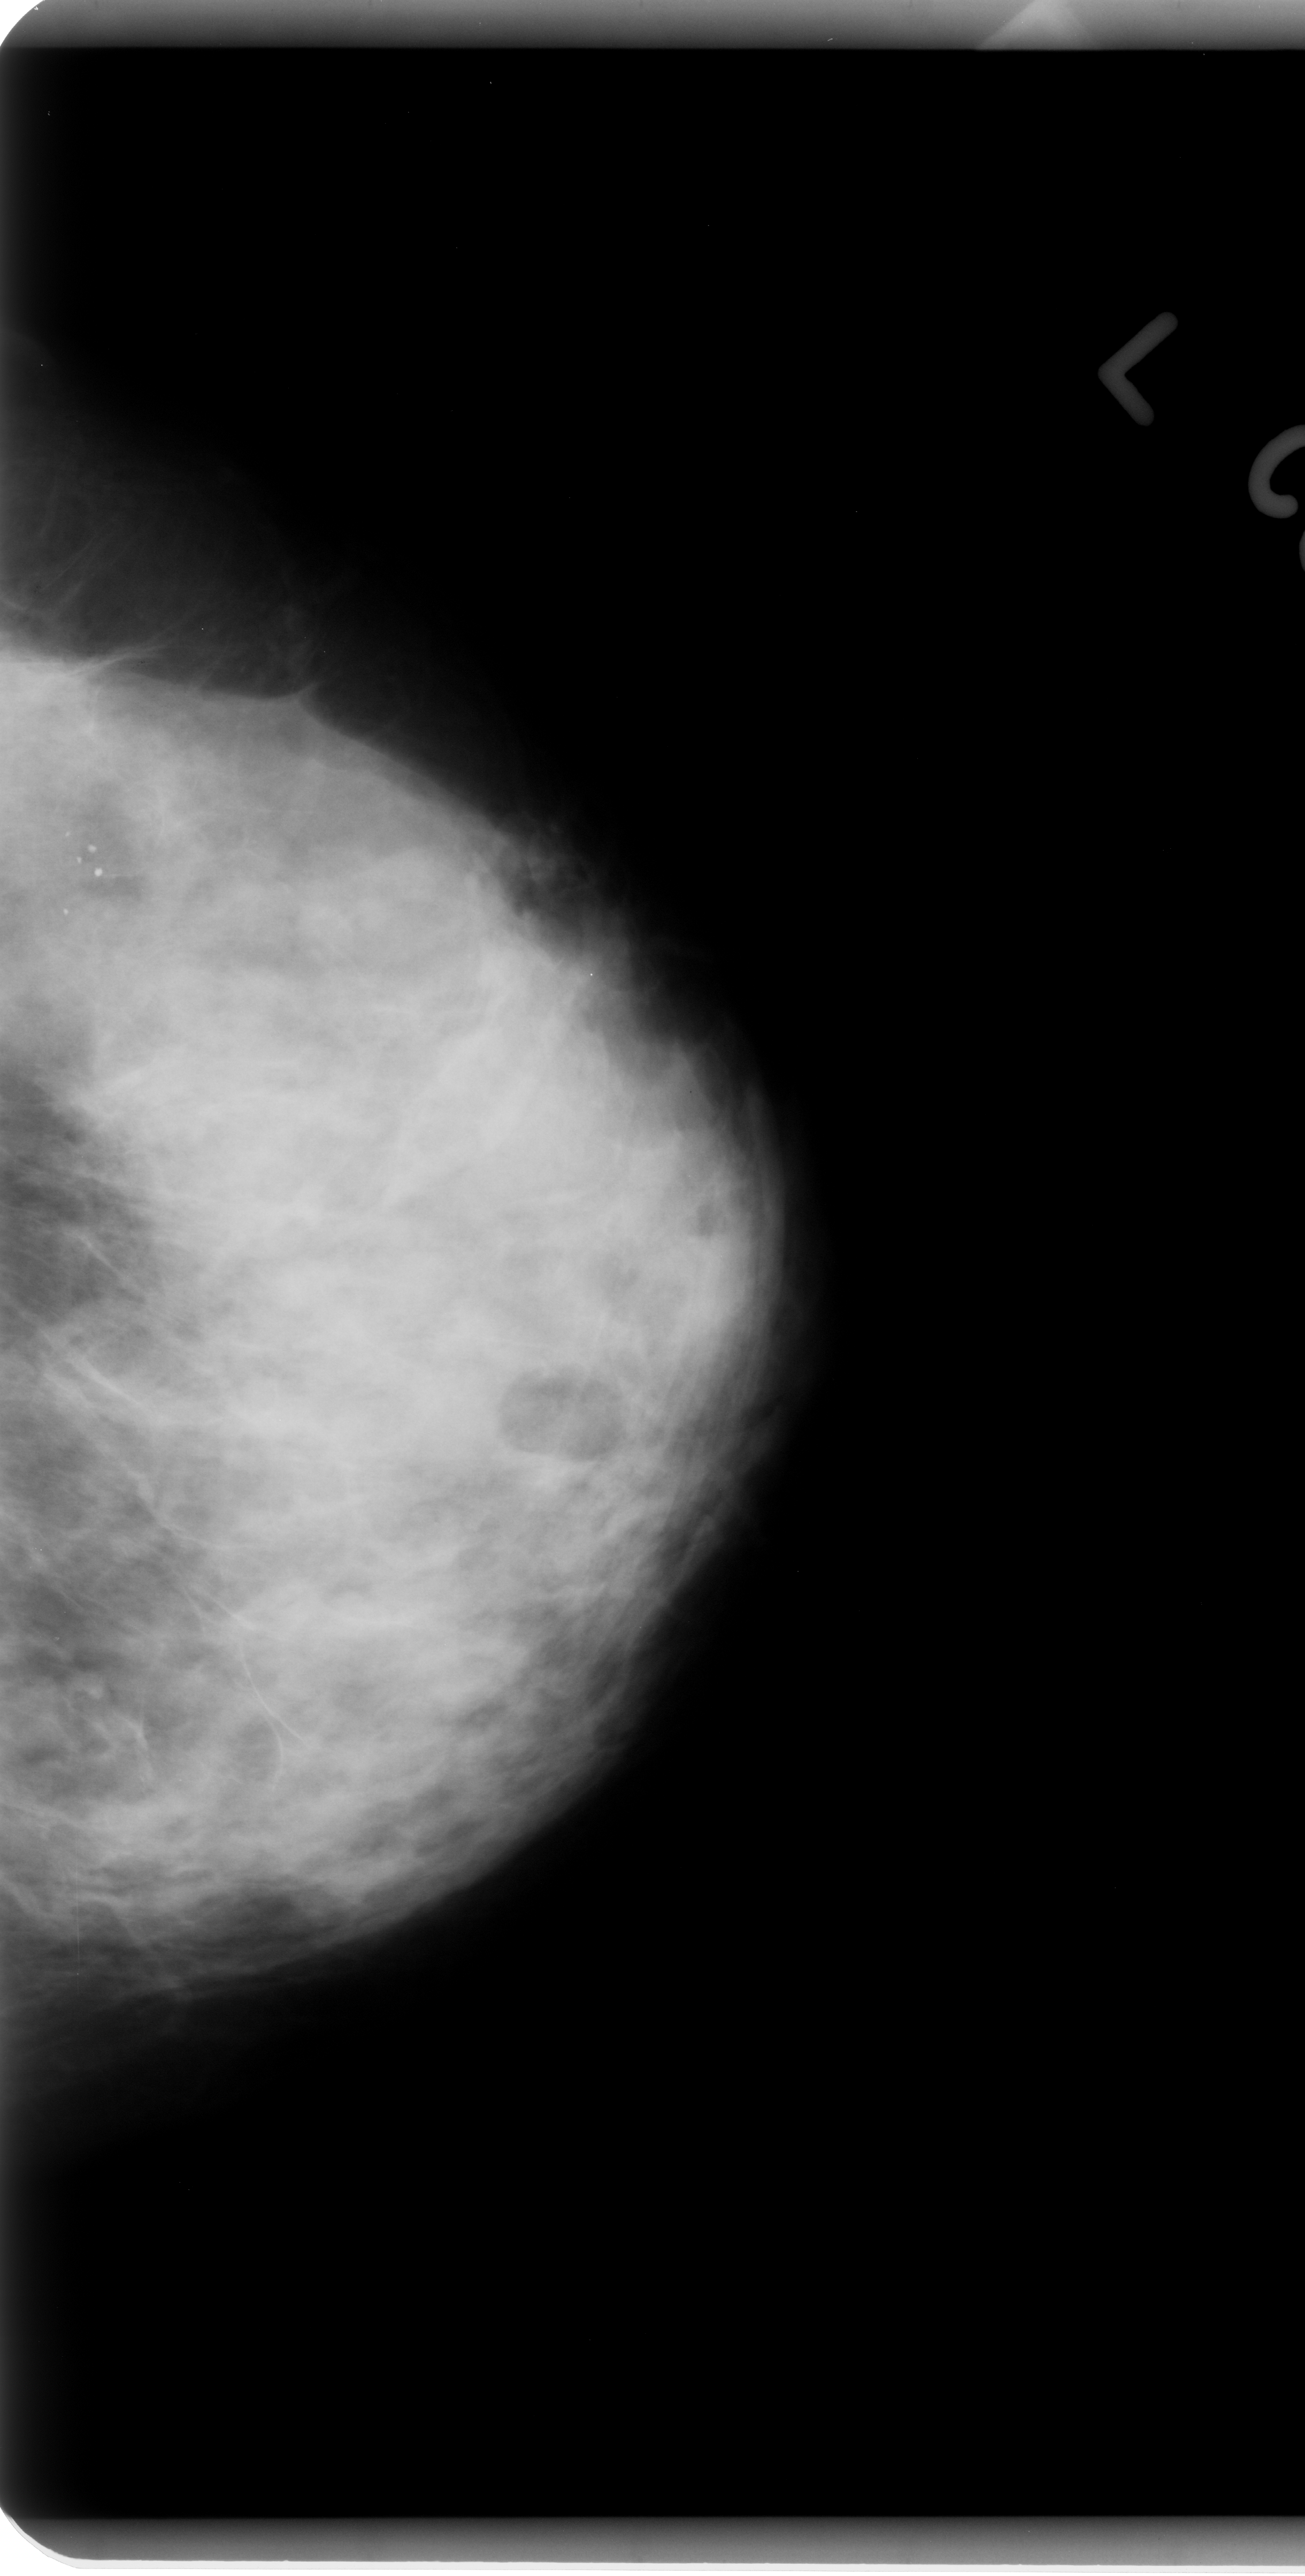
Scanned film-screen mammogram; left breast; craniocaudal (CC) view; breast composition: heterogeneously dense (BI-RADS density category 3 of 4); 1305 × 2576 image matrix.
Expert-marked regions of interest on this image (one box per marked abnormality):
- calcifications, morphology pleomorphic, distribution clustered; BI-RADS assessment category 4; pathology result (as recorded, not read from the image): benign: bounding box <12,774,129,955> (left, top, right, bottom; pixels)